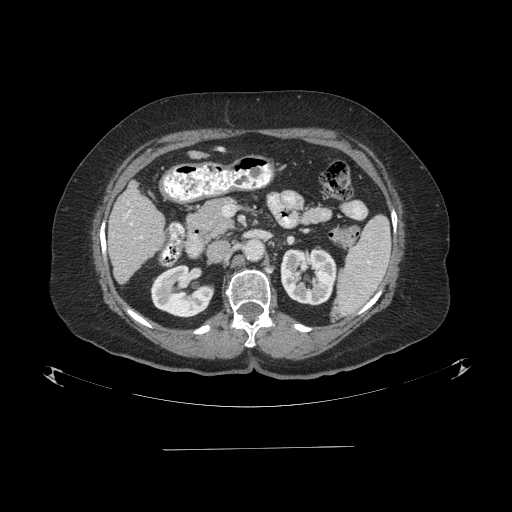
Contrast-enhanced abdominal CT (liver protocol), one axial slice. Position 36 of 103 along the scan axis. Reconstruction kernel STANDARD. 120 kVp. One of 2 acquisitions stored at this slice position. Soft-tissue window (W 400 / L 40 HU). 512 × 512 image matrix. From the clinical record (not read from this slice): diagnosis: hepatocellular carcinoma (patient treated with transarterial chemoembolisation; whether this scan precedes or follows treatment is not stated here); TNM stage (as recorded): Stage-IIIA; Child-Pugh class: A; tumour nodularity: multinodular; tumour size: 5.2 cm.
Outlined on this slice (semi-automatically segmented with operator editing):
- liver parenchyma outside the tumour (the mass and vessels are separate outlines, so this box may not span the whole liver): bounding box (x1, y1, x2, y2) in pixels: (108, 182, 164, 284)
- liver vessels: (125, 211, 142, 238)